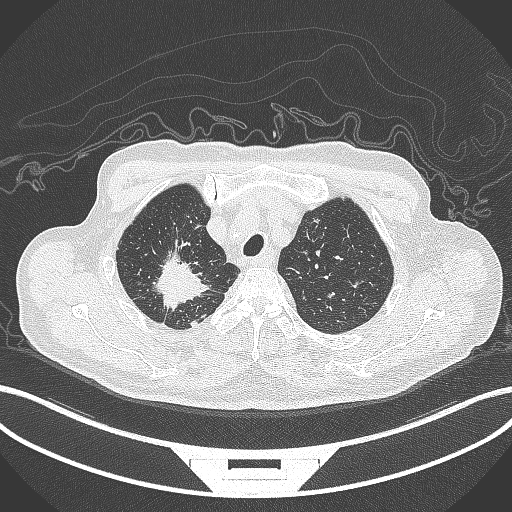
Chest CT, one axial slice. Slice 321 of 407 in the series (ordered by position). Reconstruction kernel B70f. Lung window (W 1500 / L -600 HU). 512 × 512 image matrix, field of view 400 × 400 mm. Patient: male, 69 years. From the clinical record (not read from this slice): clinical TNM (as recorded): T1c N1 M1.
Structures marked on this image (rectangle marked by the reading radiologist):
- lung tumour (recorded histology: adenocarcinoma): bounding box <148,242,219,314> (left, top, right, bottom; pixels)